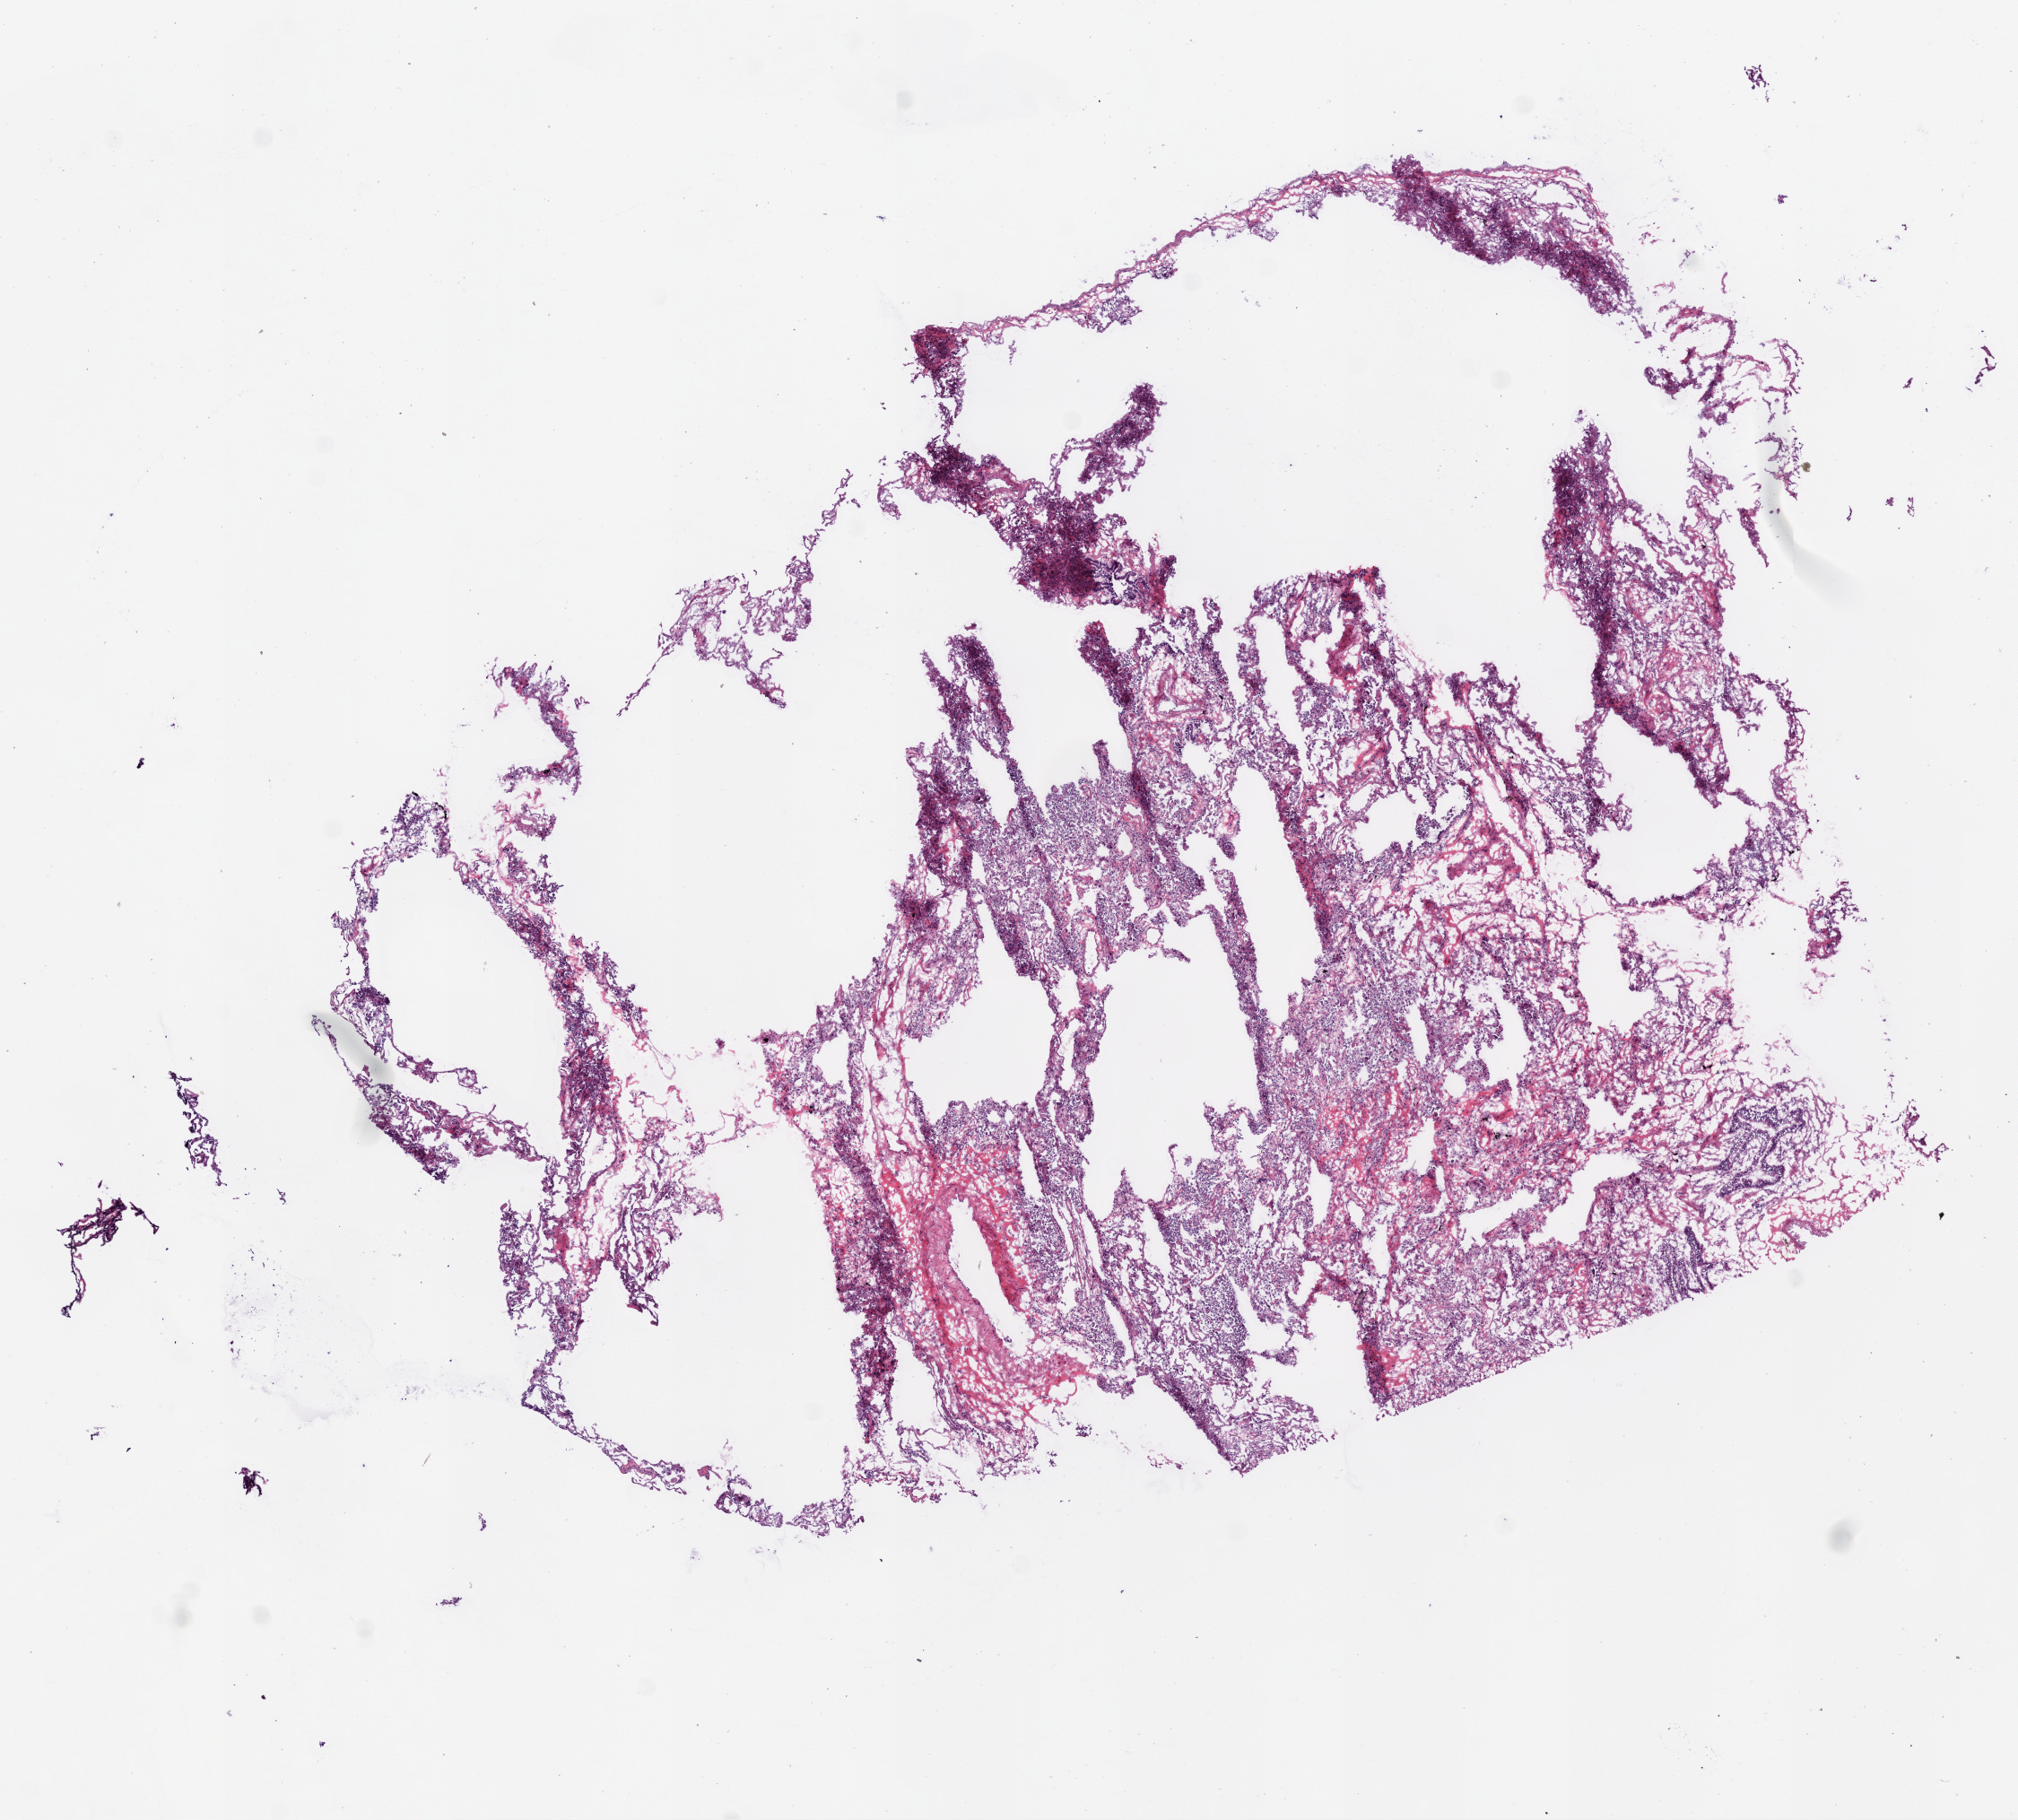
H&E-stained whole-slide image — a low-resolution overview of the entire scanned area, about 9.0 x 8.1 mm (acquisition: 20x scan), frozen section from the bottom of the tissue portion, solid tissue normal (non-tumour tissue) sample from the lung. Male patient; age at initial diagnosis 73 years.
* this section: solid tissue normal sample (biorepository sample class)
* patient diagnosis: Squamous cell carcinoma, NOS (lower lobe, lung)